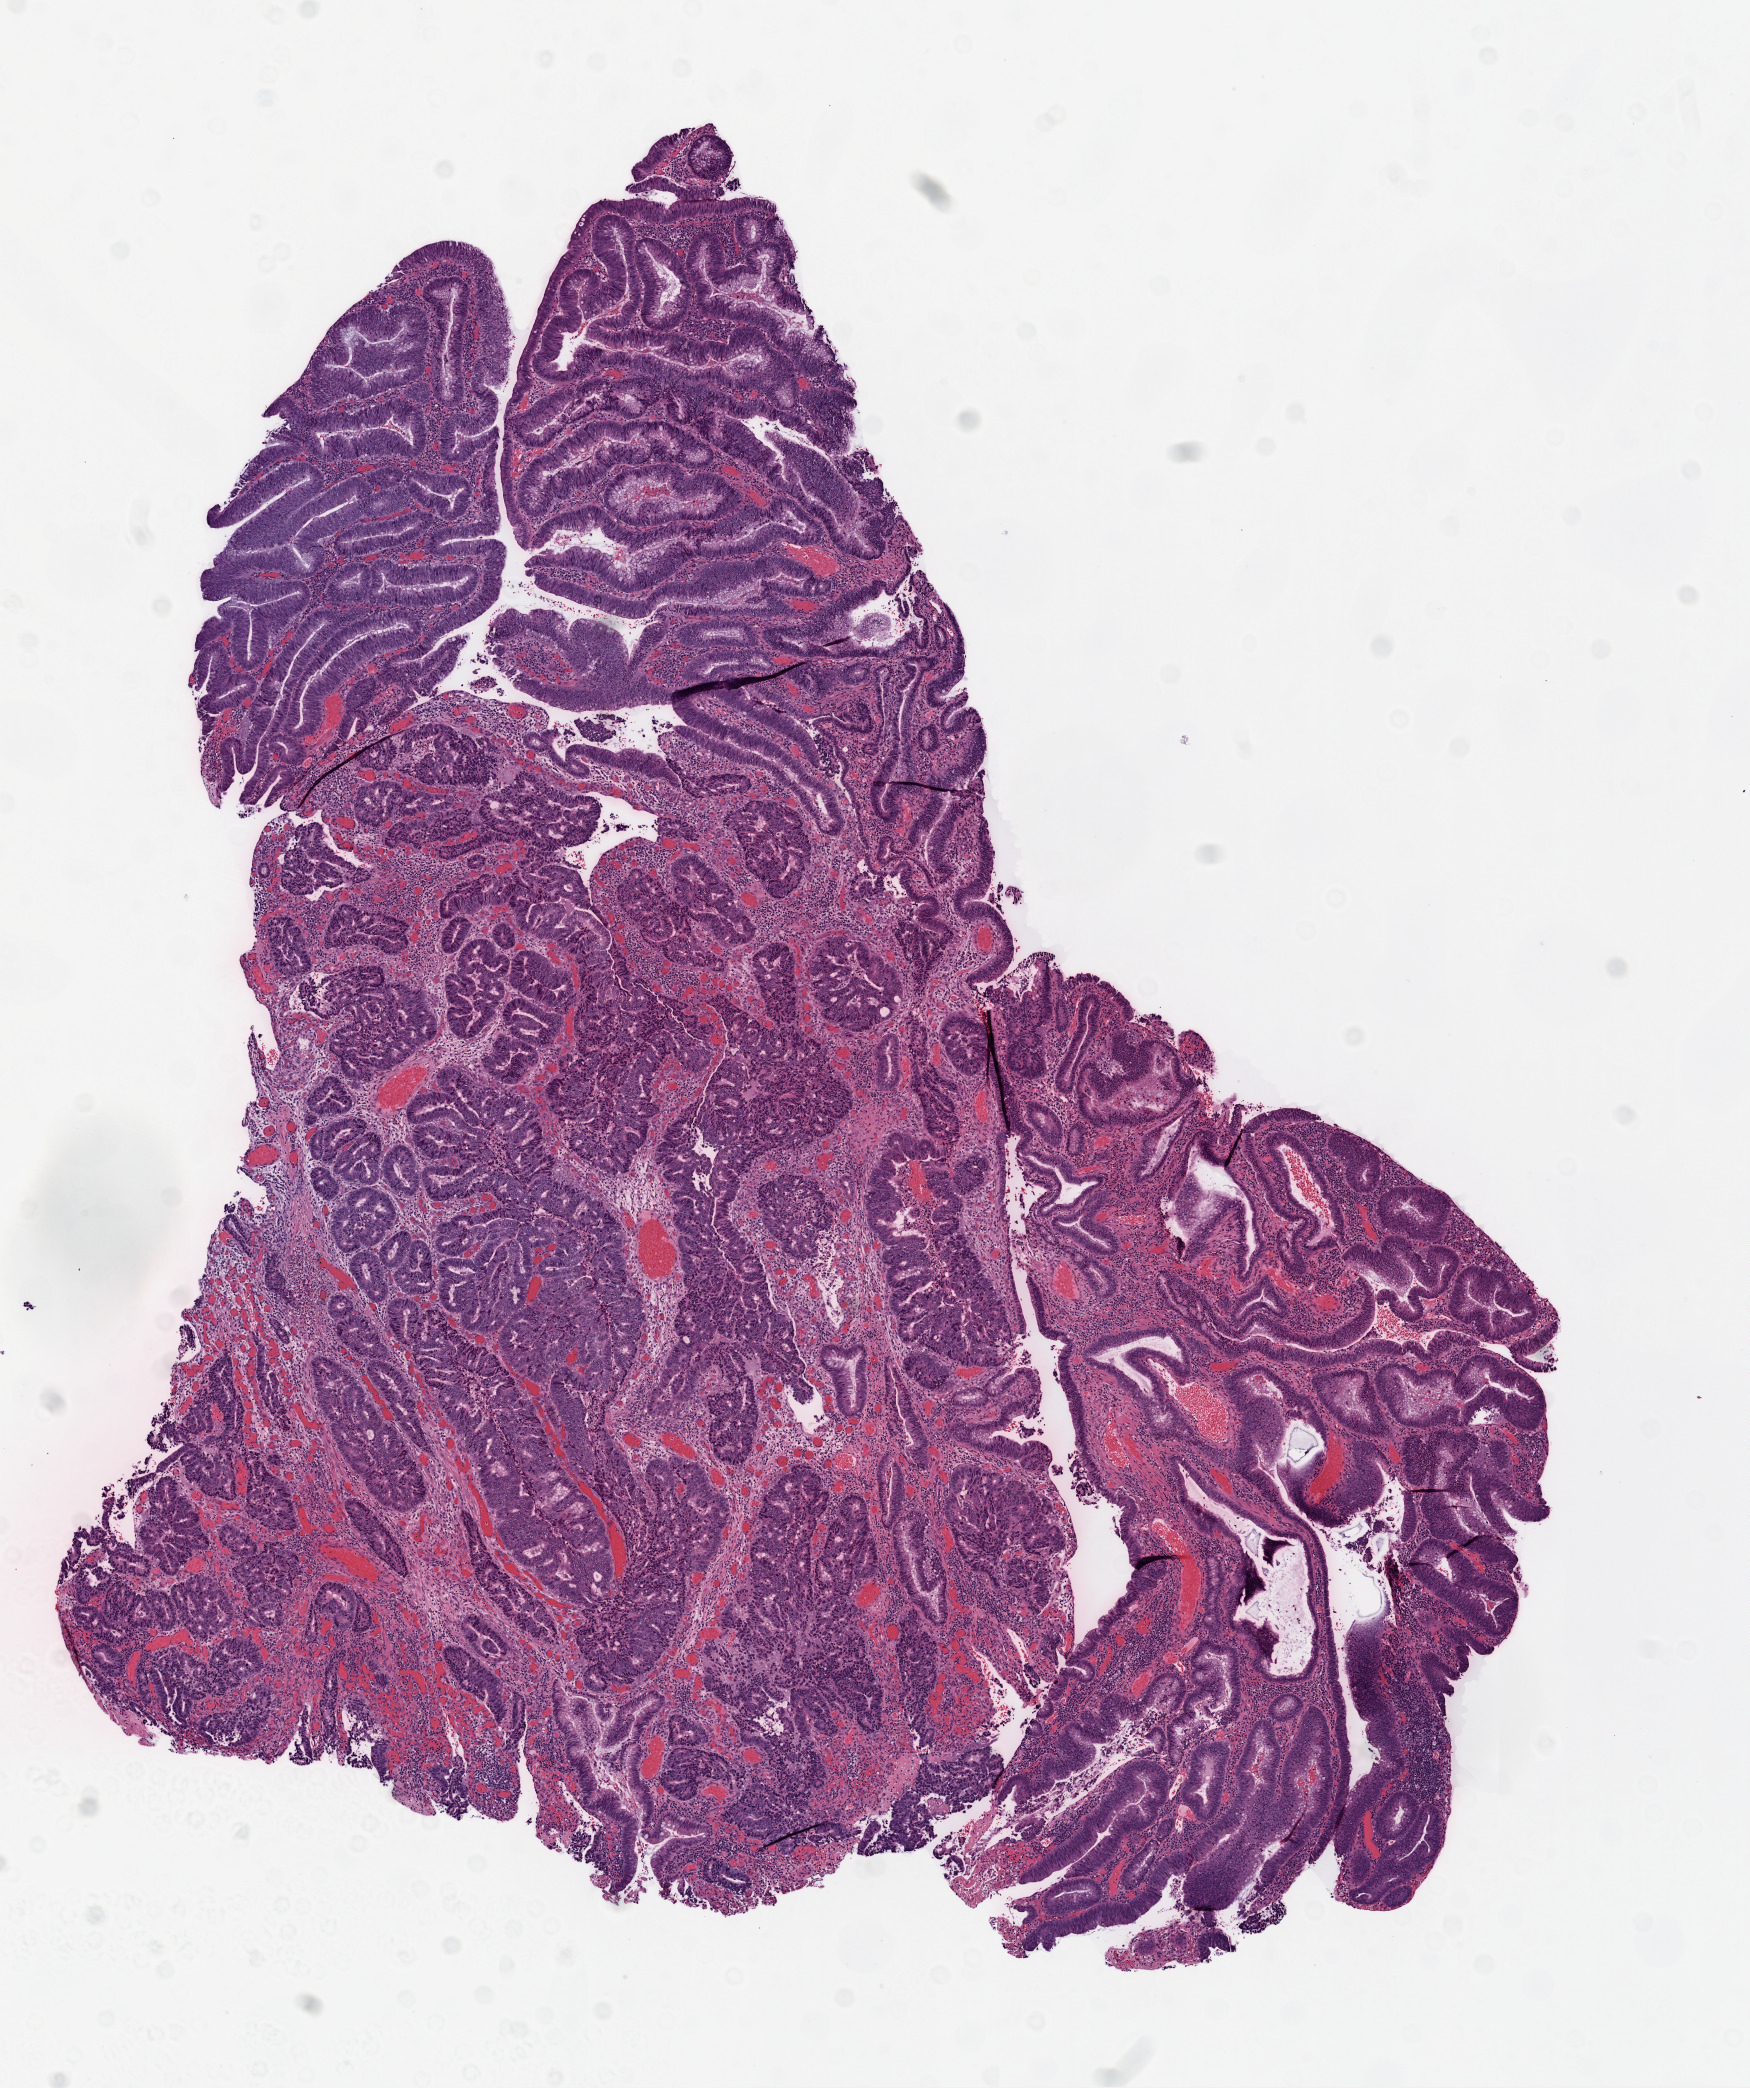
Whole-slide histology image, Hematoxylin and eosin (H&E) stained, shown as a low-resolution overview of the whole scanned area (about 7.0 x 8.4 mm, from a 20x scan). Frozen section from the top of the tissue portion. Primary tumour sample from the rectum. Patient: female, age at initial diagnosis 41 years. Slide review estimates, as recorded: tumour cells 89%, tumour nuclei 80%, normal cells 0%, stromal cells 10%, necrosis 1%.
* AJCC pathologic stage: IV
* lymph nodes positive (case pathology): 6 of 32 examined
* pathologic diagnosis: Adenocarcinoma, NOS (rectosigmoid junction)